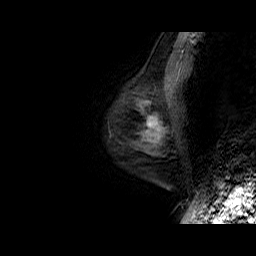
Breast MRI (dynamic contrast-enhanced), one sagittal slice; dynamic contrast-enhanced series, time point 2 of 6 at this slice position (early post-contrast); 1.5 T; TE 6.5 ms, TR 32.9 ms; 4 mm slice thickness; 256 × 256 image matrix, field of view 200 × 200 mm. Female patient. From the clinical record (not read from this slice): setting: breast cancer imaged before/during neoadjuvant chemotherapy; receptor status: HR-positive, HER2-negative.
Annotated regions visible in this slice (semi-automatically segmented with operator editing):
- analysis volume of interest (the breast-tissue region the enhancement analysis was run in; not a lesion): bounding box (x1, y1, x2, y2) in pixels: (114, 75, 179, 149)
- tumour enhancement mask (voxels above the 100 % enhancement threshold inside the analysis volume of interest): (147, 117, 160, 141)